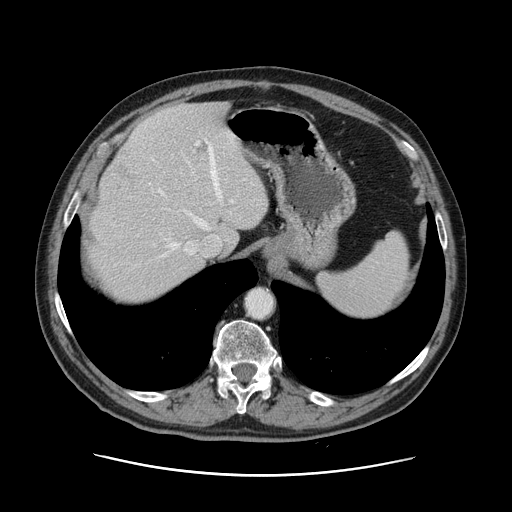
Contrast-enhanced abdominal CT, one axial slice. Slice 101 of 141 in the series (ordered by position). 120 kVp. Intravenous contrast given. Soft-tissue window (W 400 / L 40 HU). 2.5 mm slice thickness. 512 × 512 image matrix, field of view 395 × 395 mm. Male patient, age 72 years. From the clinical record (not read from this slice): diagnosis: colorectal cancer liver metastases, imaged before liver resection; multiple liver metastases: yes; largest metastasis: 5.4 cm; chemotherapy before resection: yes.
Annotated regions visible in this slice (outlined manually by an expert reader):
- hepatic veins: bounding box <152,140,221,257> (left, top, right, bottom; pixels)
- liver: <91,102,269,306>
- planned liver remnant (the part of the liver to remain after resection): <96,102,269,306>
- portal vein (with intrahepatic branches): <190,142,233,250>
- liver metastasis: <113,159,130,182>